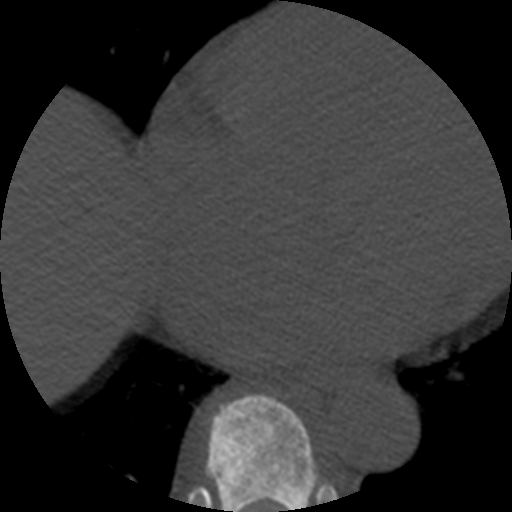
CT including the spine, one axial slice. Position 316 of 508 along the scan axis. Reconstruction kernel STANDARD. Bone window (W 1800 / L 400 HU). 1.25 mm slice thickness. 512 × 512 image matrix, field of view 160 × 160 mm. Patient age 57 years. Case-level facts recorded for this patient, not image findings: primary cancer: prostate.
Annotated regions visible in this slice (semi-automatic segmentation, software-assisted and operator-edited):
- T8 vertebra: box from (x=206, y=393) to (x=318, y=512) px